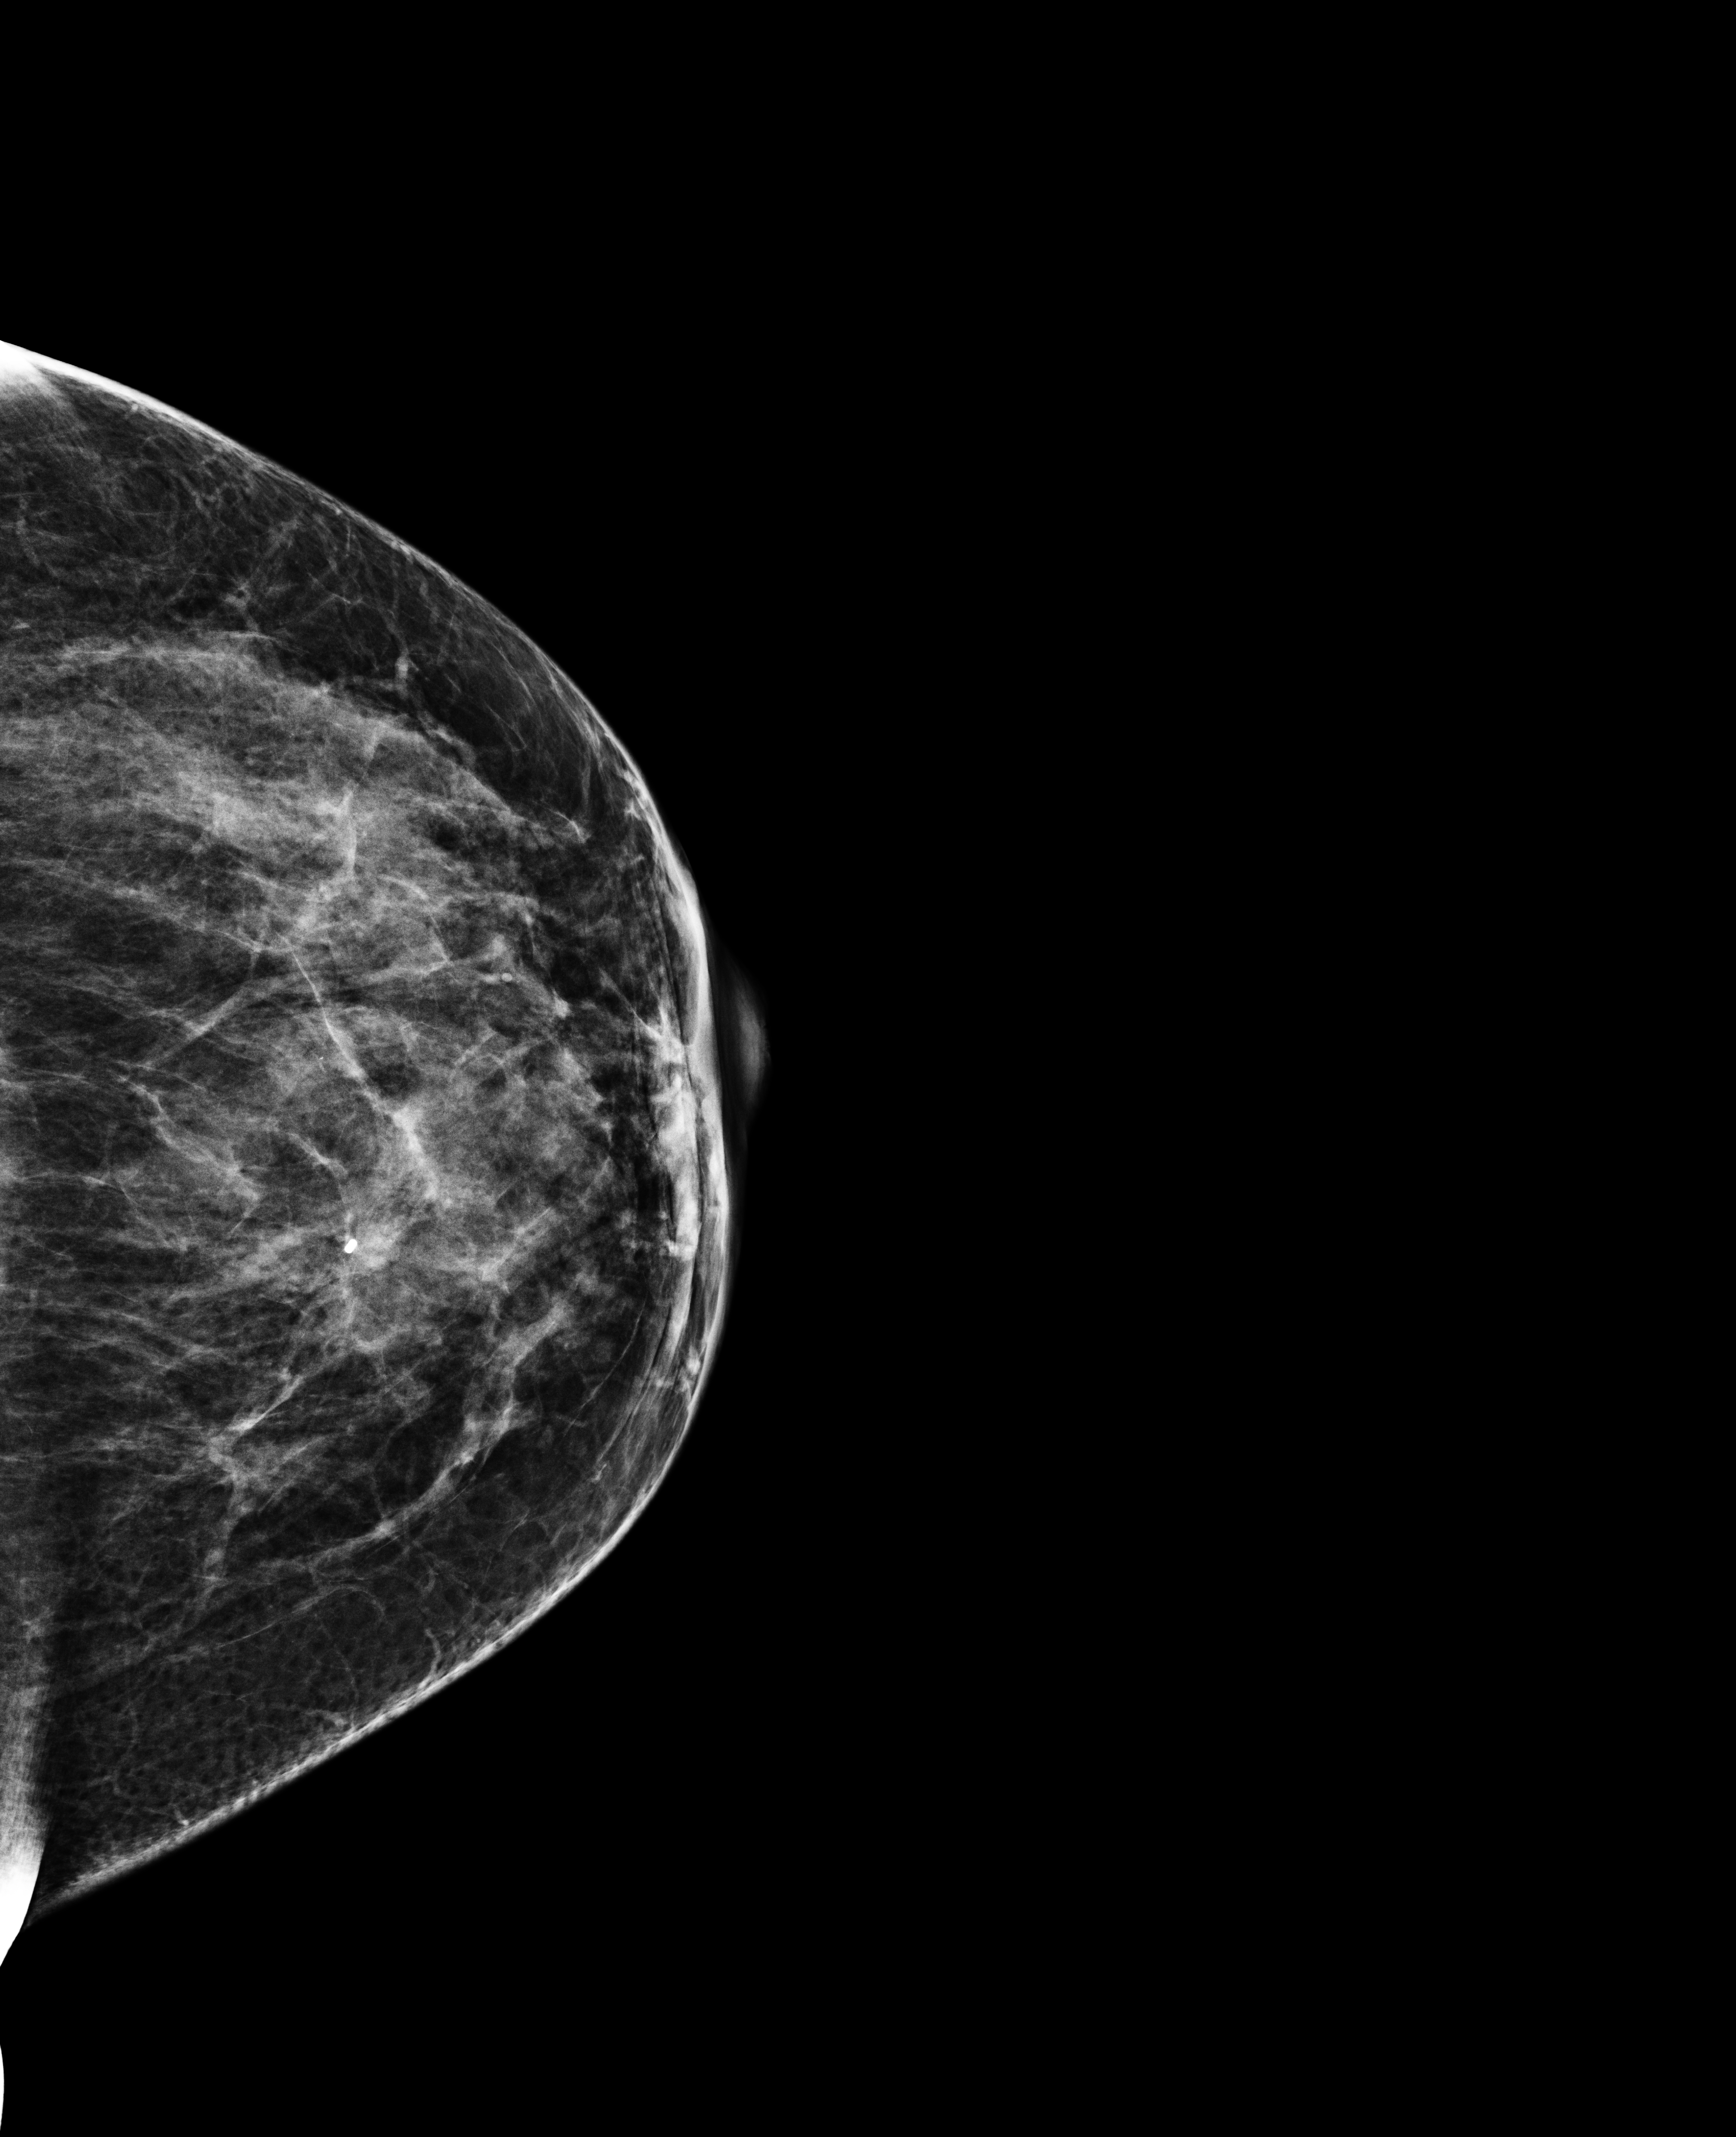
Screening examination. Patient: female, 43 years.
Image type: full-field digital mammogram. Breast: left. Projection: cranio-caudal projection.